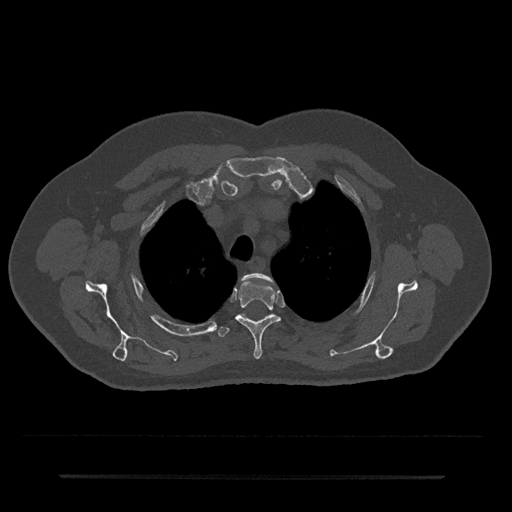
CT including the spine, one axial slice. Reconstruction kernel Br40s/3. 120 kVp. Bone window (W 1800 / L 400 HU). 0.5 mm slice thickness. 512 × 512 image matrix. Patient: male, 69 years. From the clinical record (not read from this slice): primary cancer: prostate.
Outlined on this slice (semi-automatic segmentation, software-assisted and operator-edited):
- T2 vertebra: bounding box (x1, y1, x2, y2) in pixels: (242, 273, 272, 283)
- T3 vertebra: (235, 278, 280, 359)
- T4 vertebra: (218, 314, 245, 337)